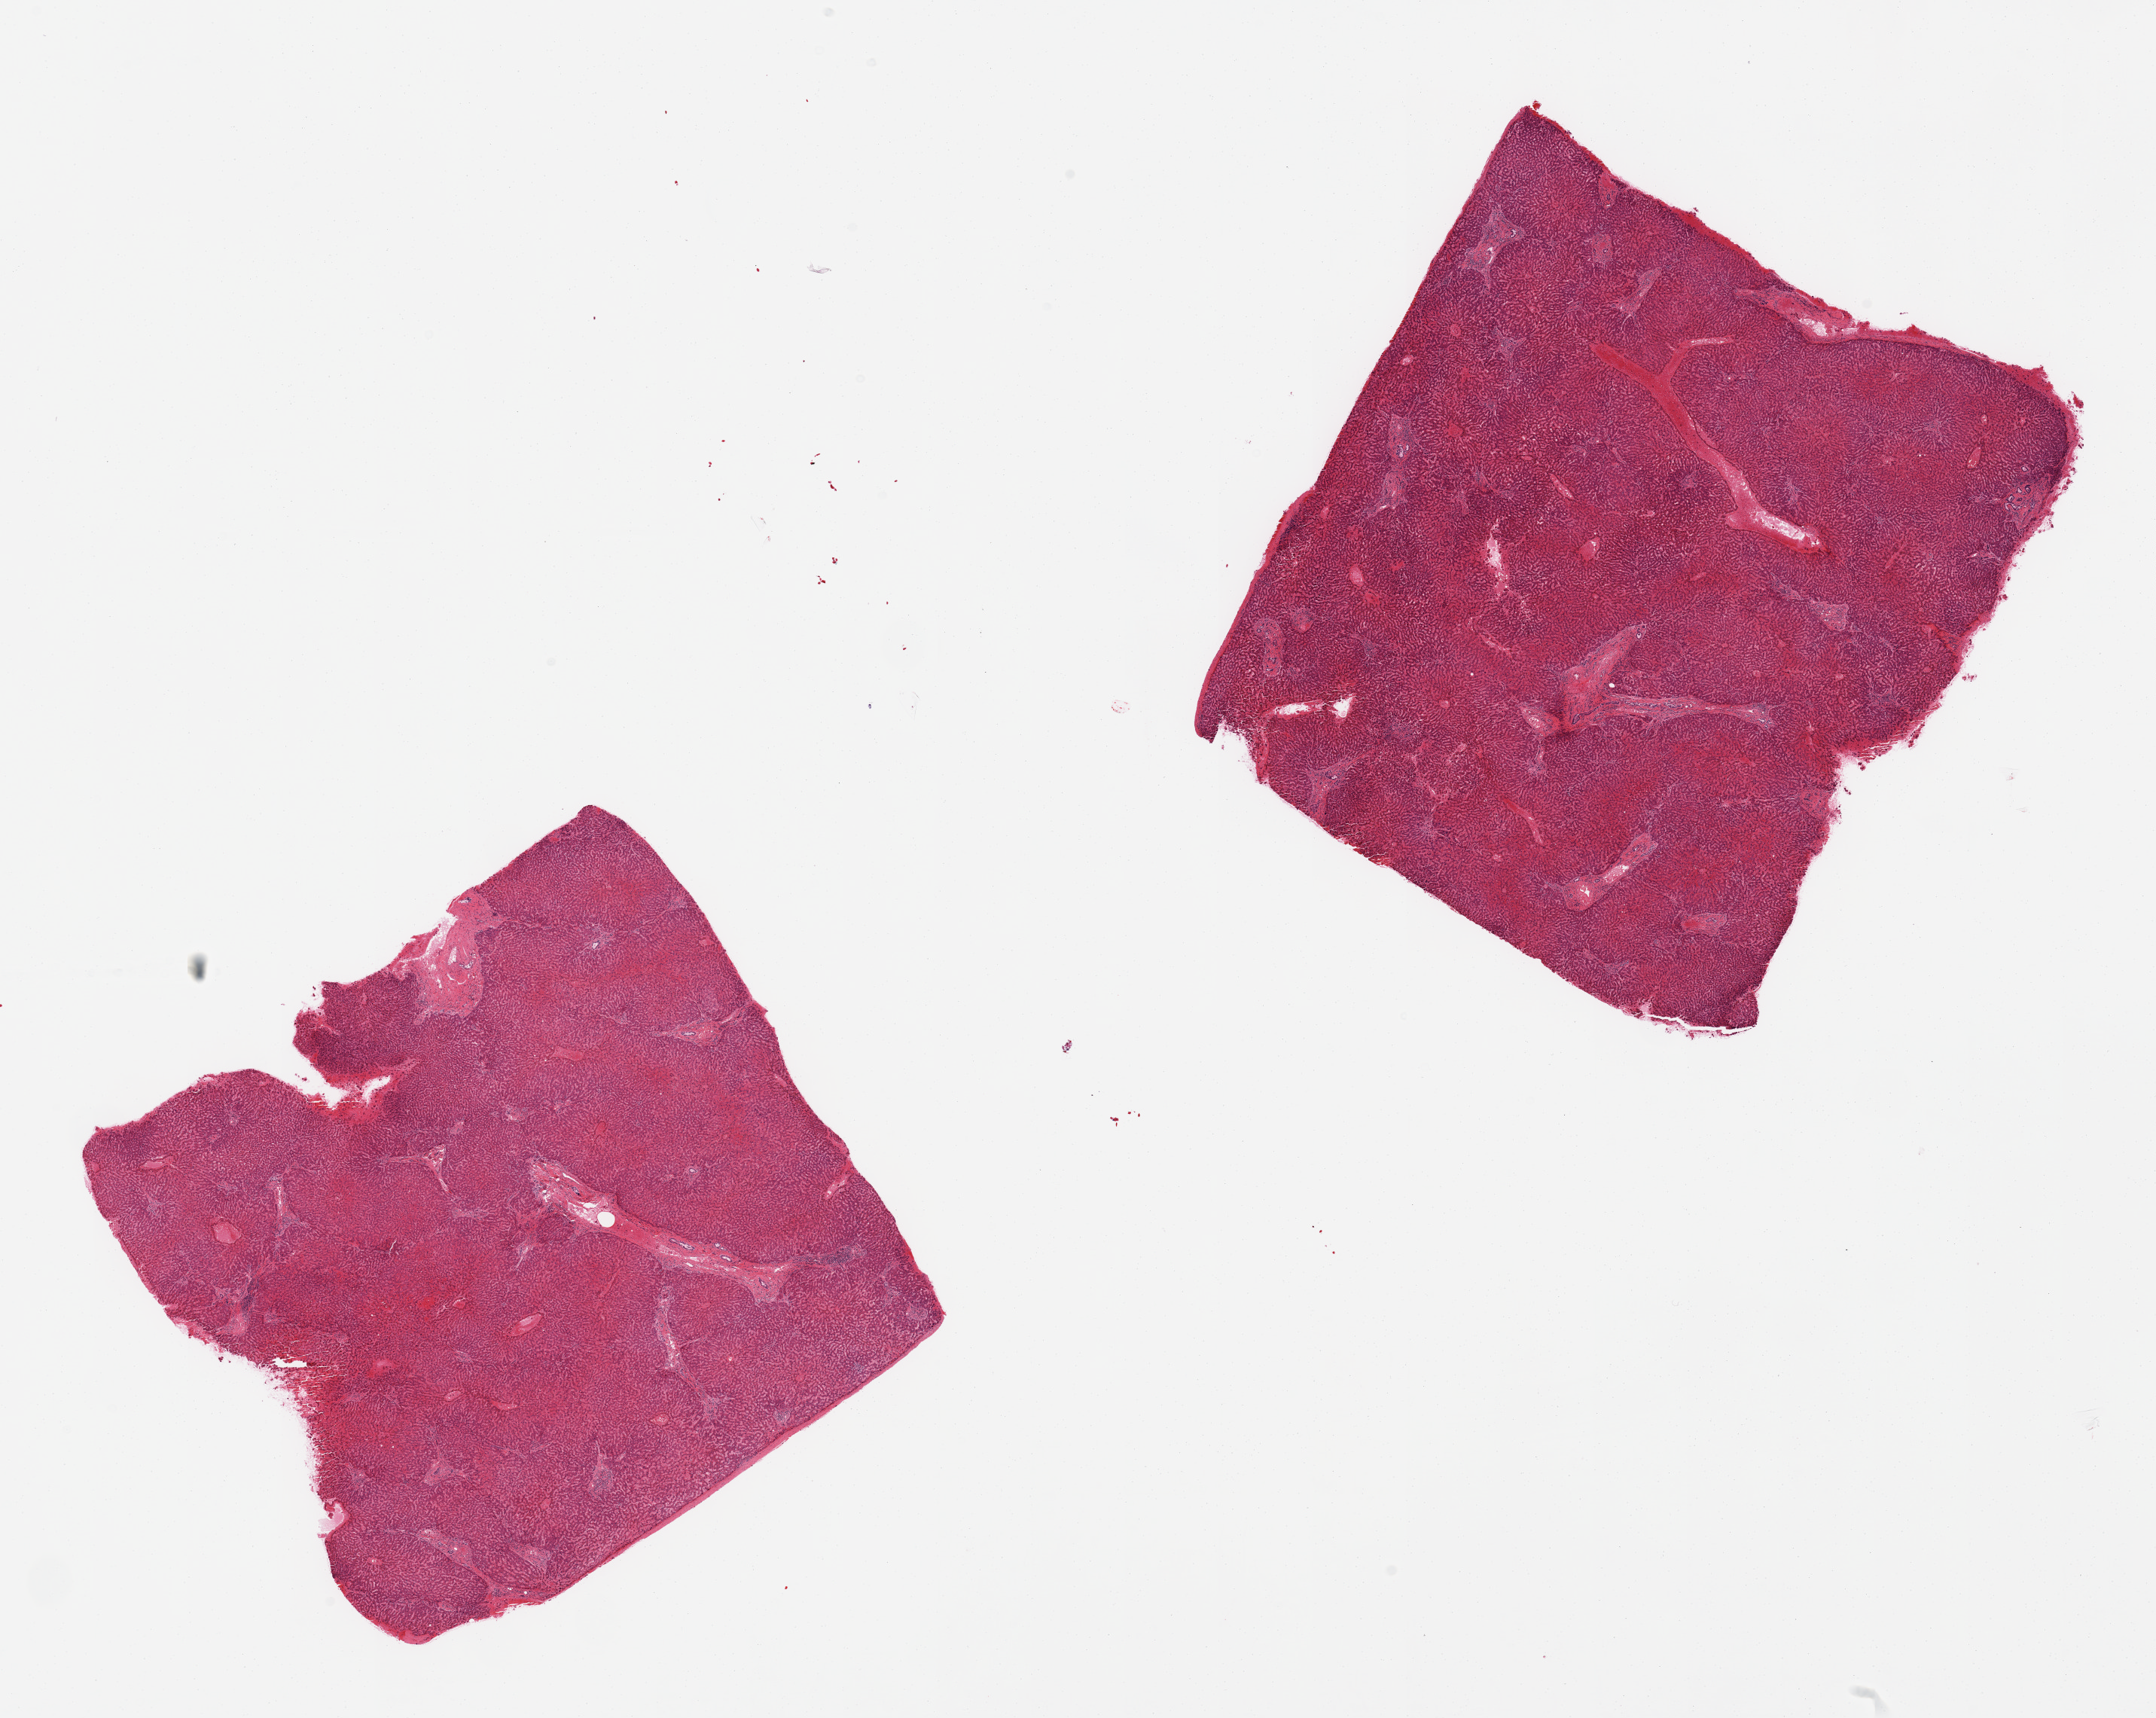
Hematoxylin and eosin (H&E) whole-slide image, brightfield, low-resolution overview of the scanned area, about 22.6 x 18.0 mm (slide scanned at 20x); PAXgene-fixed, paraffin-embedded tissue; sampled site (target tissue): liver; tissue donor sample.
Review note (as recorded): 2 pieces, congested, includes capsule (target is 1 cm below capsule), chronic inflammation.